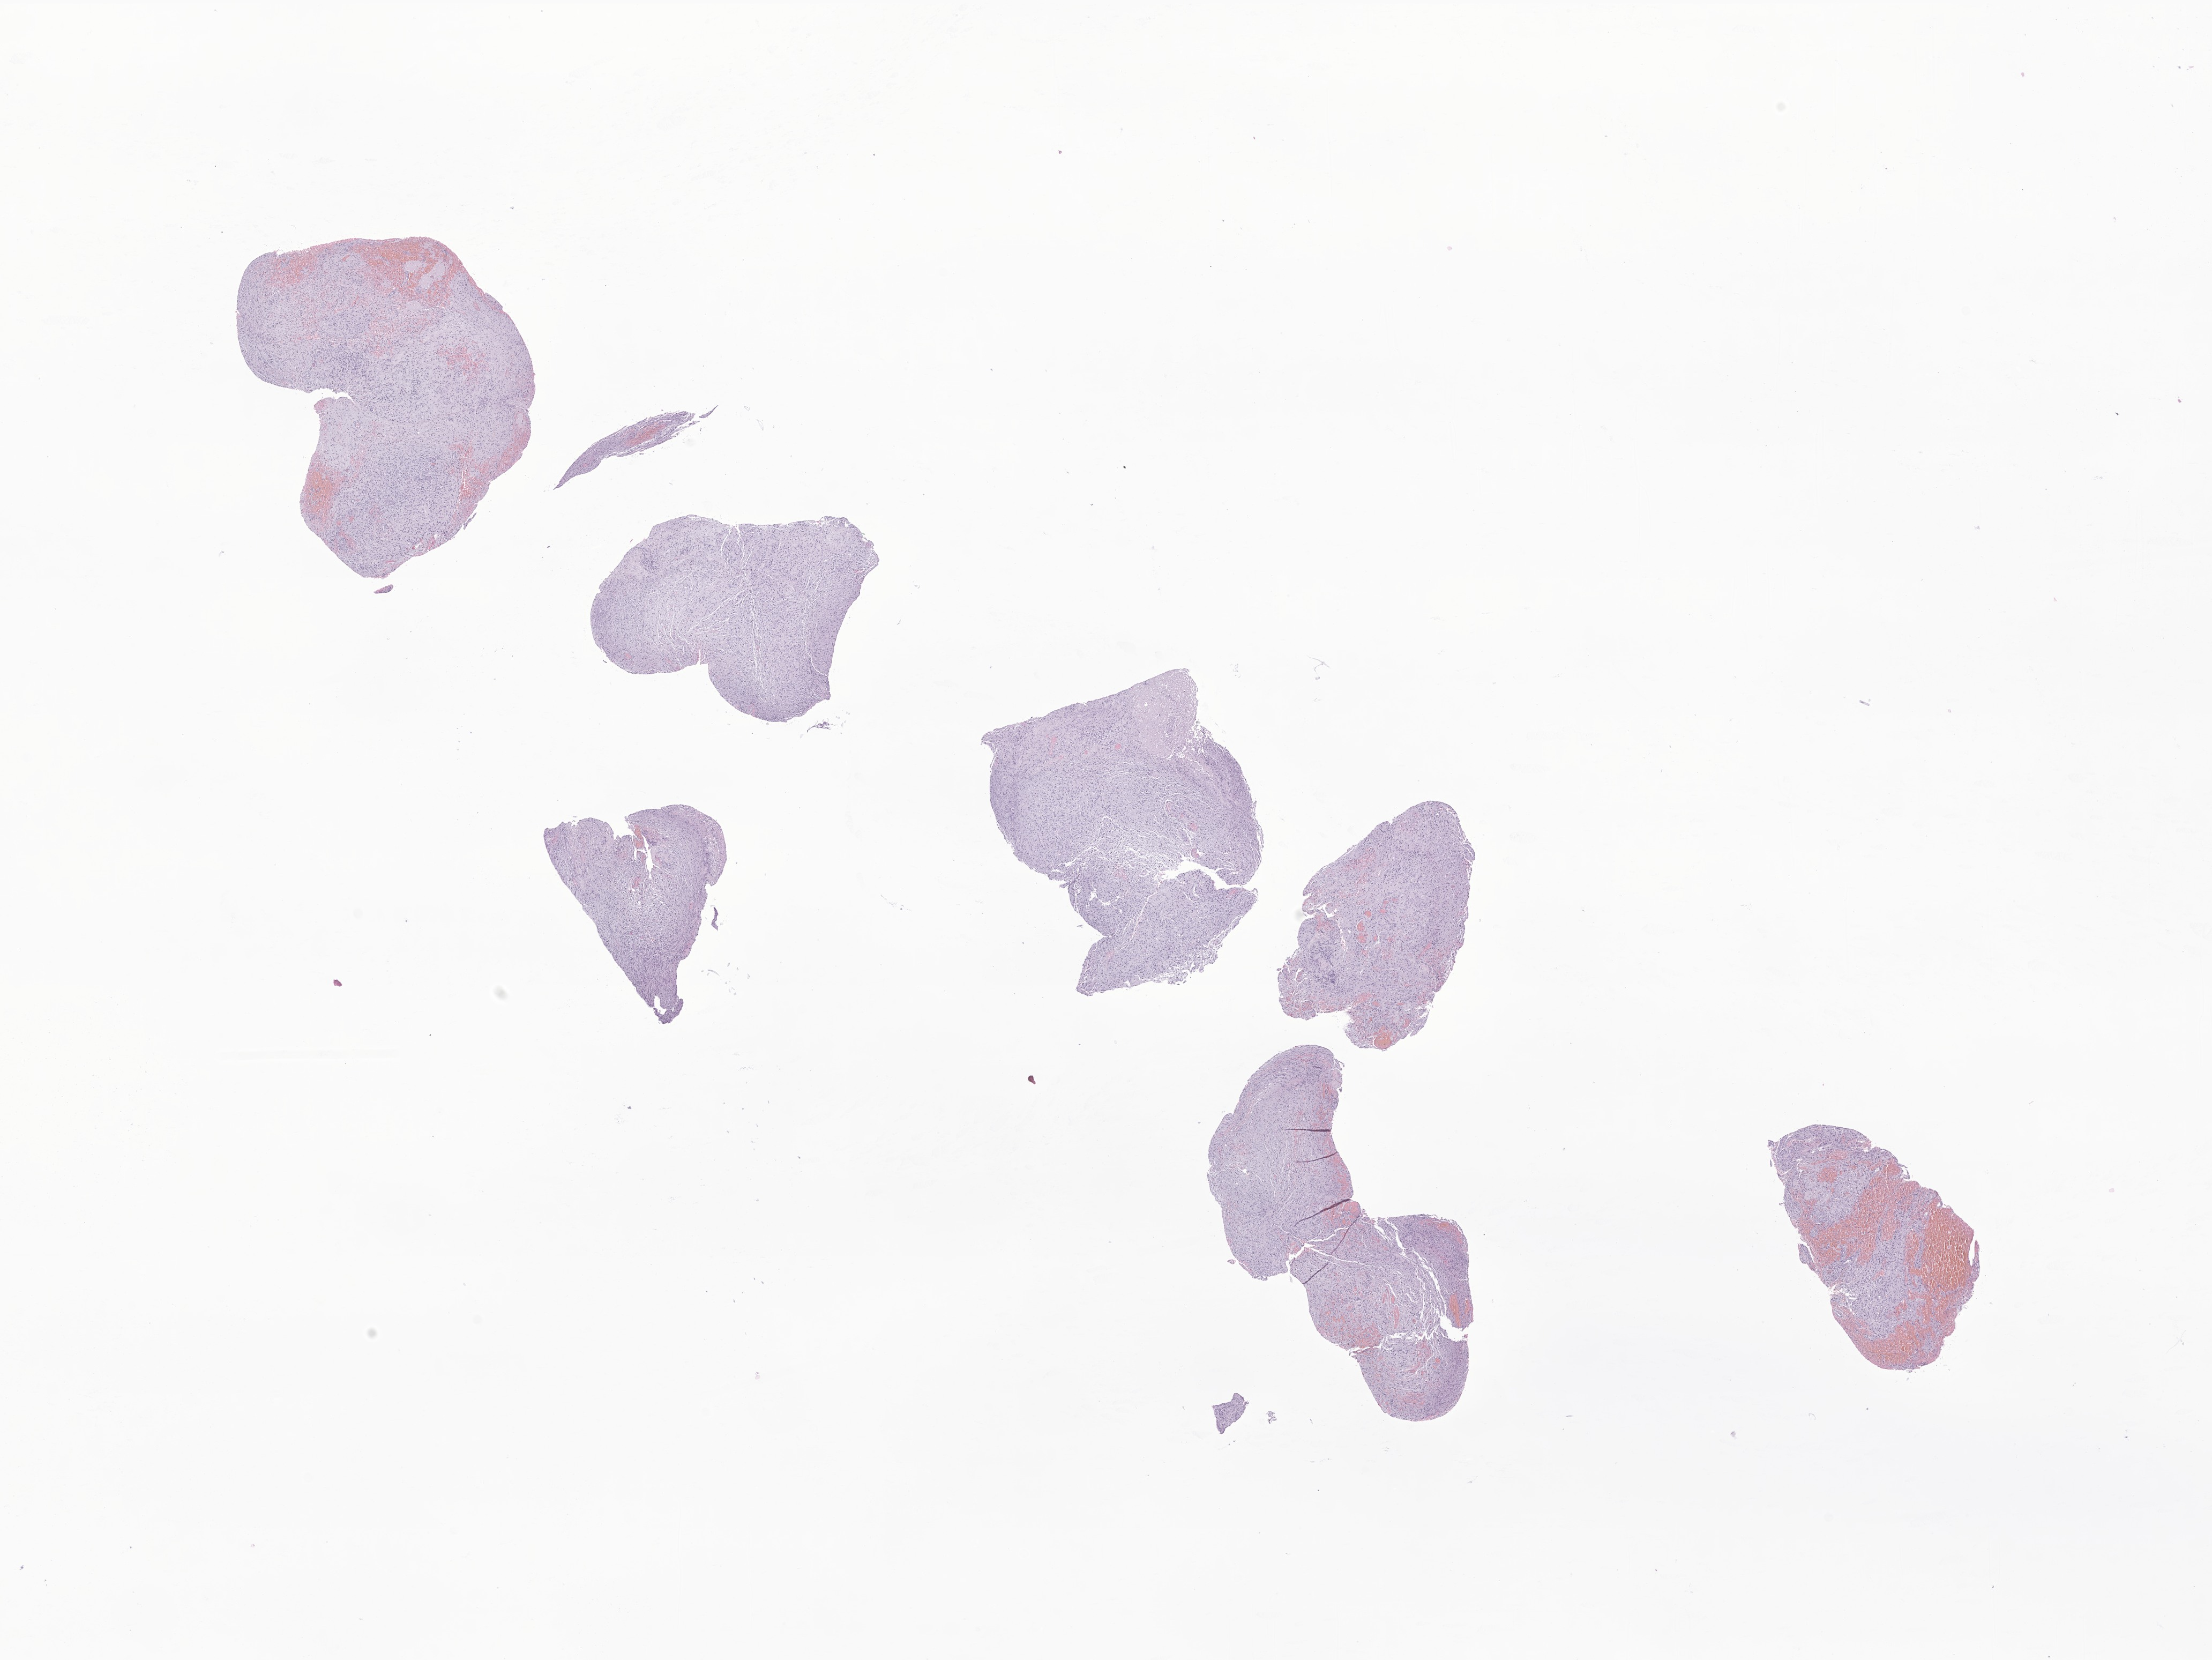
Hematoxylin and eosin (H&E) whole-slide image of tumor tissue from the spinal cord — whole scanned area (about 17.4 x 13.1 mm) shown as a low-resolution overview; formalin-fixed, paraffin-embedded (FFPE) tissue. Patient: male, age 113 months (9 years 5 months).
- diagnosis: Astrocytoma, NOS